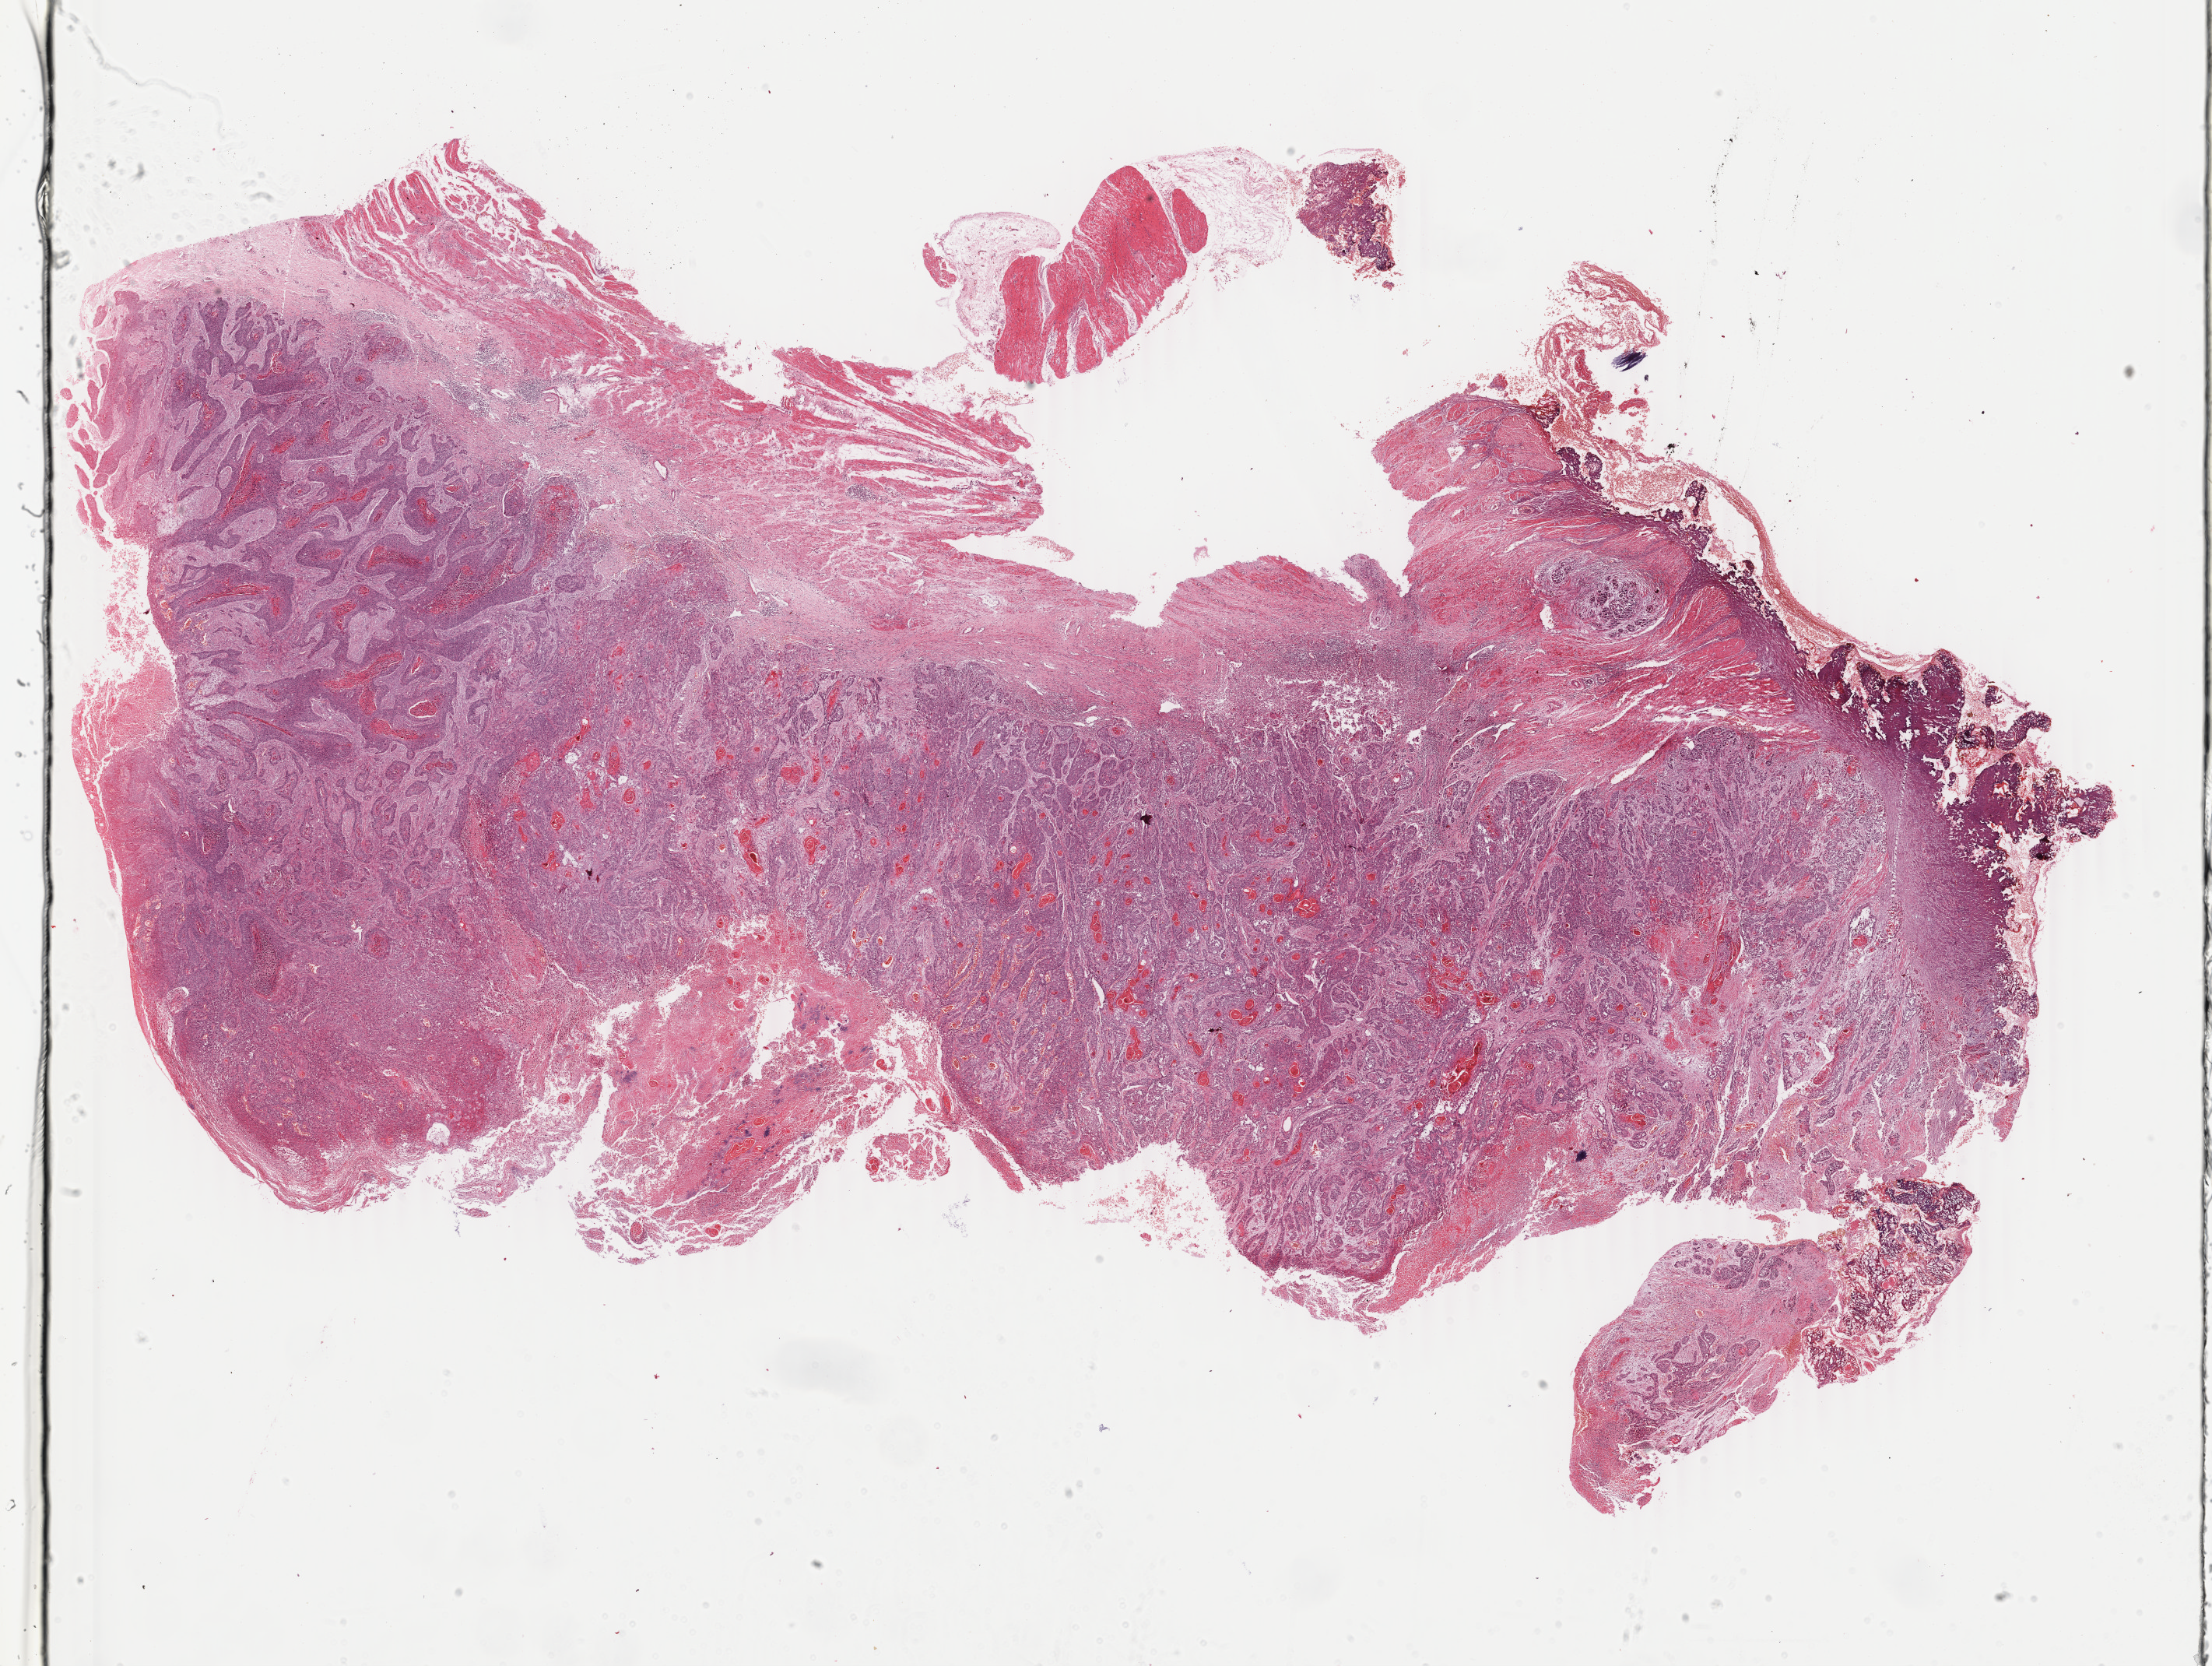
Digitized Hematoxylin and eosin (H&E) stained tissue section (whole slide) — shown as a low-resolution overview of the whole scanned area (about 22.6 x 17.0 mm, acquisition: 40x scan). Formalin-fixed paraffin-embedded (FFPE) diagnostic section. Esophagus, primary tumour sample. Male patient; age at initial diagnosis 46 years. Histologic grade: G3 (poorly differentiated).
Lymph nodes positive (case pathology): 1 of 1 examined. Pathologic diagnosis: Squamous cell carcinoma, NOS (lower third of esophagus). AJCC pathologic stage: III (6th edition).